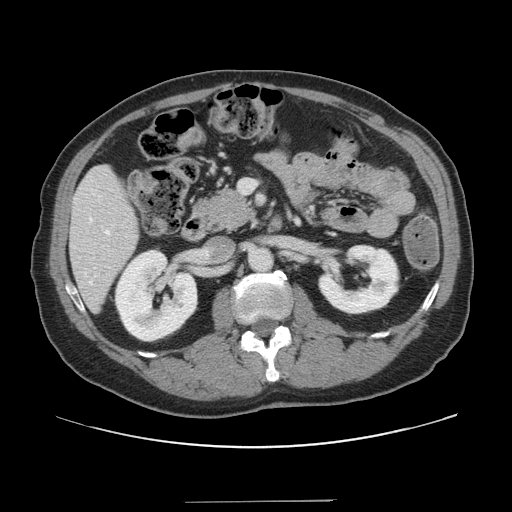
Contrast-enhanced abdominal CT, one axial slice; slice 61 of 151 in the series (ordered by position); 120 kVp; intravenous contrast given; soft-tissue window (W 400 / L 40 HU); 2.5 mm slice thickness; 512 × 512 image matrix, field of view 399 × 399 mm. Male patient, age 63 years. From the clinical record (not read from this slice): diagnosis: colorectal cancer liver metastases, imaged before liver resection; multiple liver metastases: no; largest metastasis: 2.1 cm; disease in both lobes: no.
Outlined on this slice (manually delineated by an expert):
- hepatic veins: bounding box <90,230,110,284> (left, top, right, bottom; pixels)
- liver: <72,167,139,311>
- planned liver remnant (the part of the liver to remain after resection): <71,167,138,310>
- portal vein (with intrahepatic branches): <239,180,256,194>